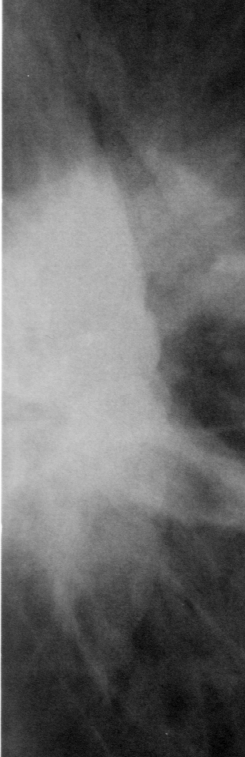
Cropped region of a digitized screen-film mammogram centred on a radiologist-marked abnormality; left breast; CC view; BI-RADS breast density category 1 (scale 1–4).
- Marked abnormality: mass, shape irregular, margins spiculated; BI-RADS assessment category 5; pathology (as recorded): malignant.